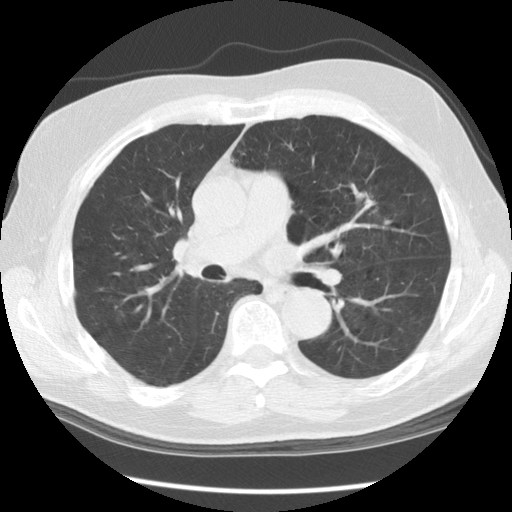
Axial slice from a low-dose chest CT screening exam, second annual screen, lung window (W 1500 / L -600 HU). Male participant, aged 70 years at enrolment. Current smoker at enrolment.
• Expert reader's lesion annotation, box from (x=339, y=177) to (x=399, y=233) px.
• The screening reader recorded 3 non-calcified nodules or masses ≥4 mm on this exam (right lower lobe, left upper lobe, left upper lobe); which of them this box marks is not recorded.
• Official screen result: positive, other.
• Lung cancer was diagnosed 396 days after this screen (after the third annual screen): adenocarcinoma, NOS, left upper lobe, moderately differentiated (G2), stage IIIA (AJCC 6th edition), 17 mm at pathology.